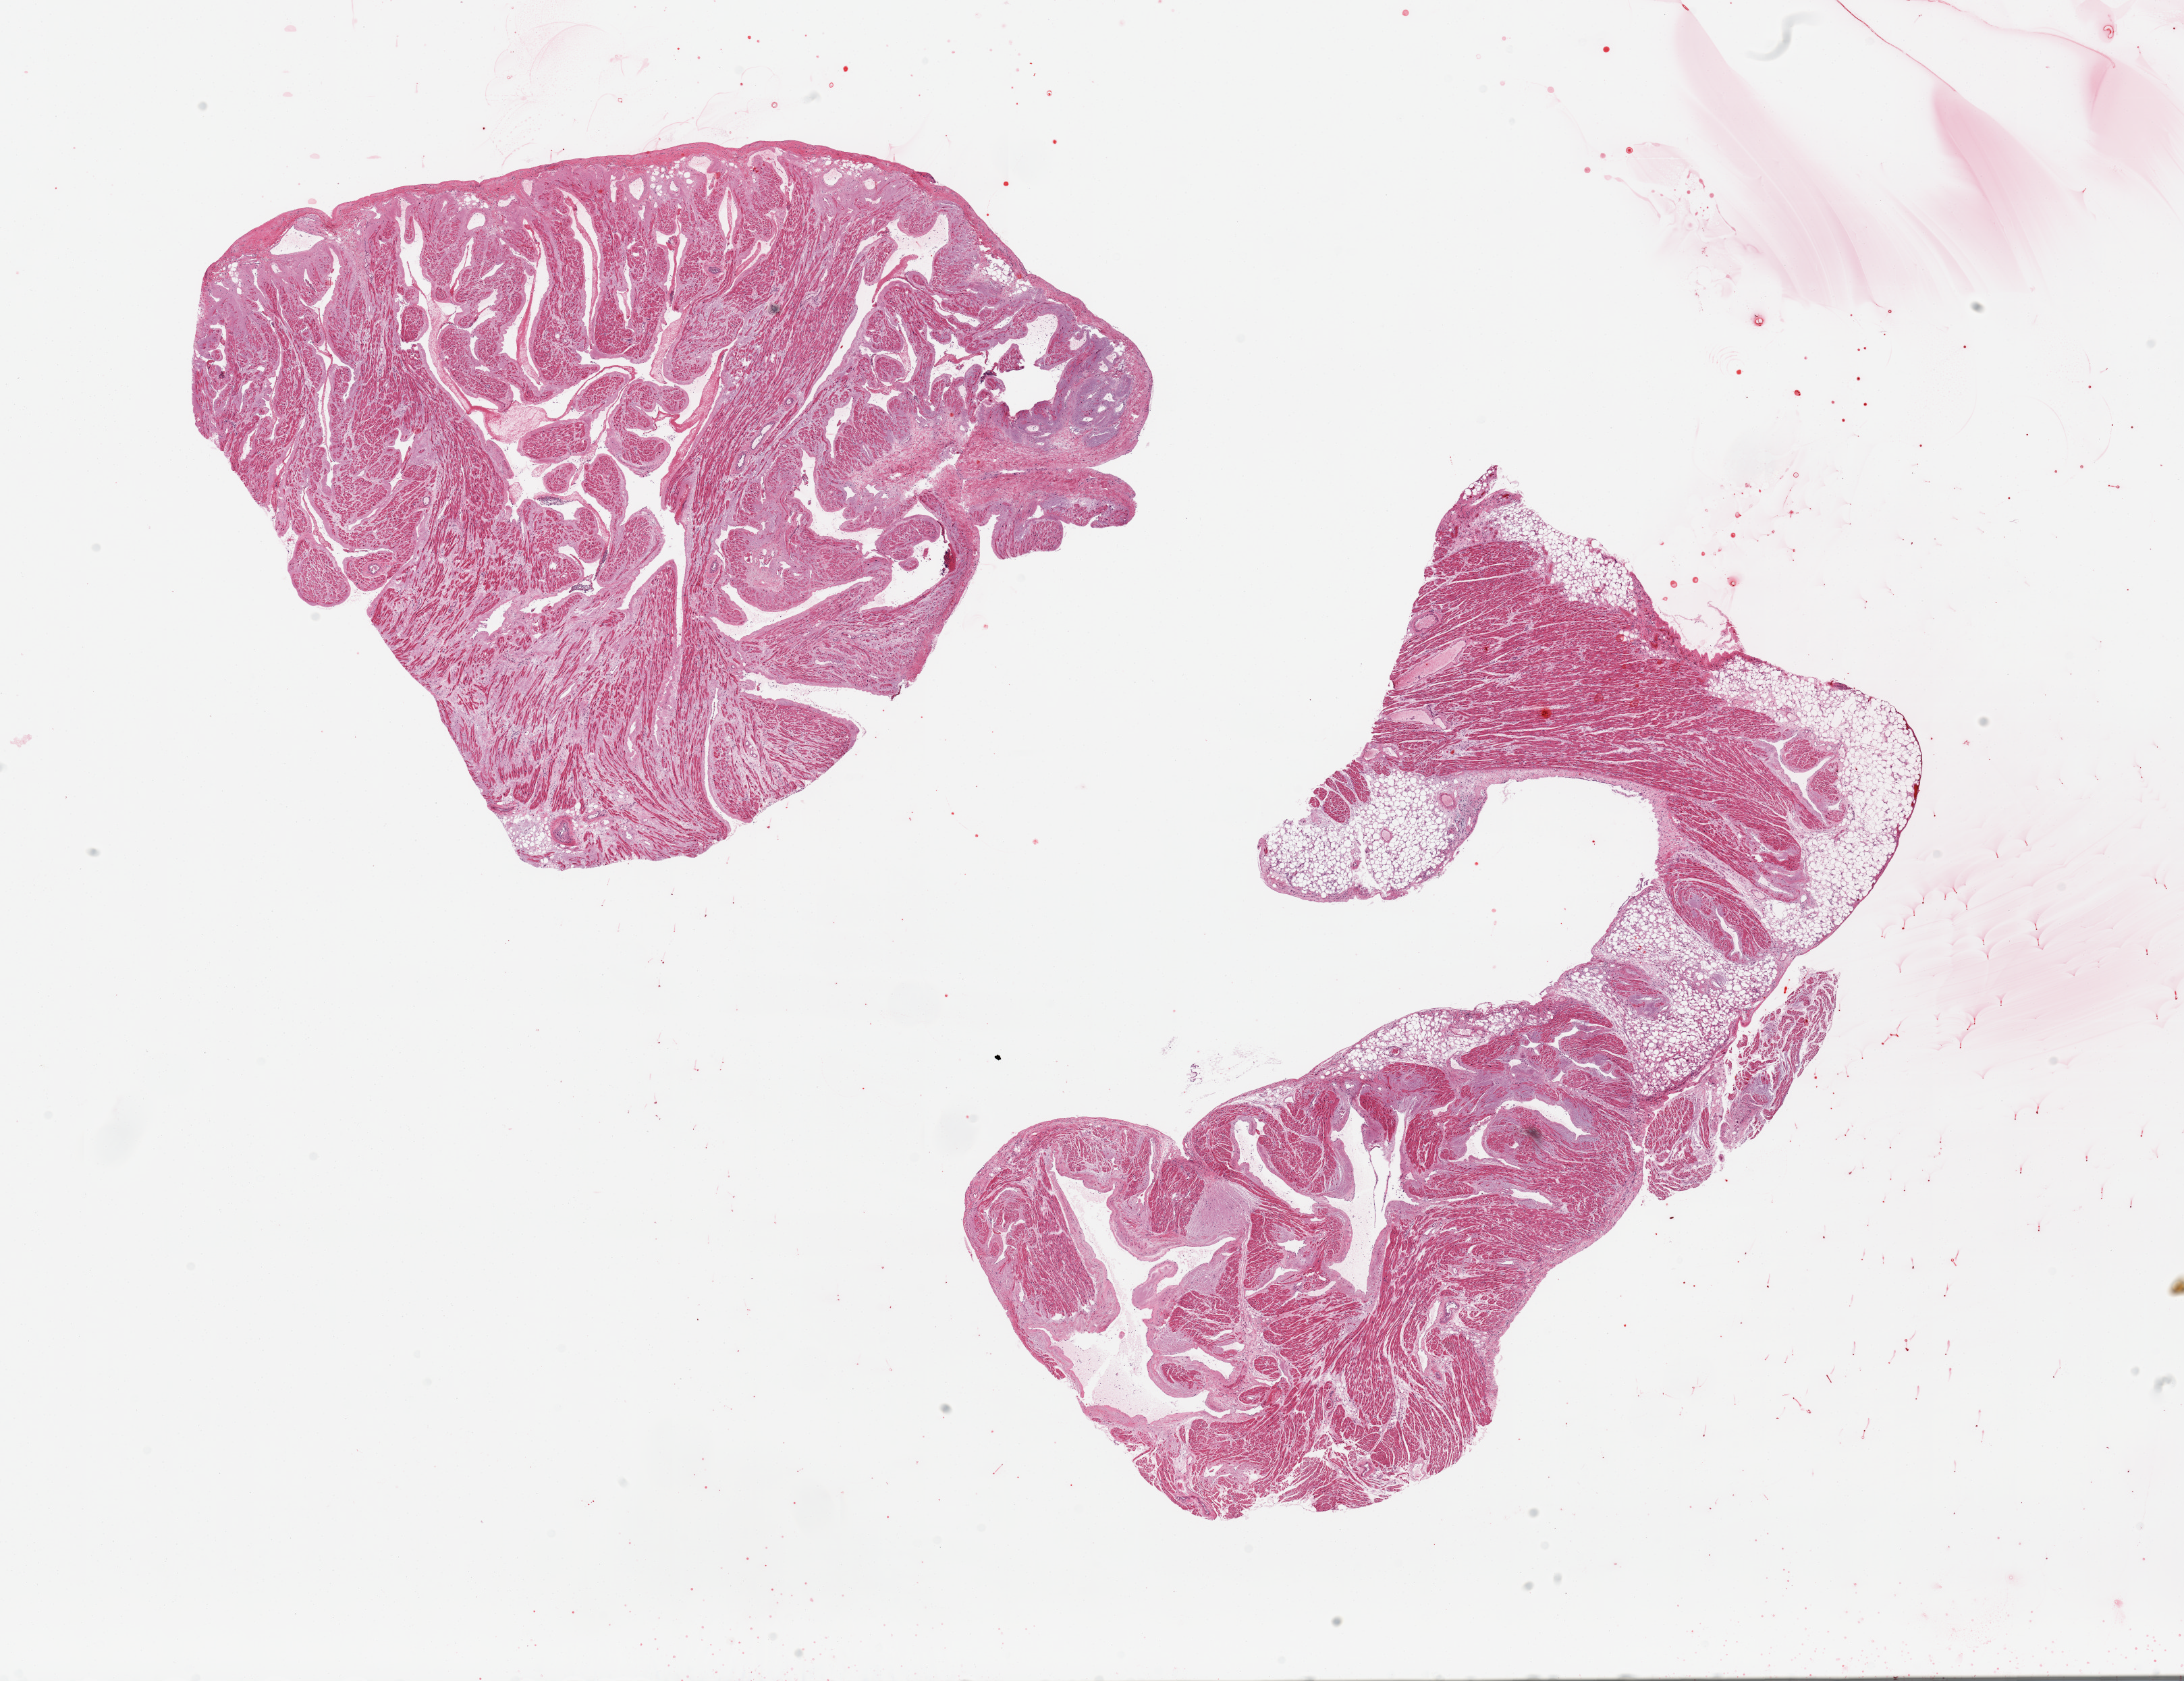
Whole-slide image, H&E stain, brightfield — low-resolution overview of the scanned area, about 25.6 x 19.7 mm. PAXgene-fixed, paraffin-embedded tissue. Section of auricular appendage (target tissue). Donor tissue sample. Donor sex: male.
Reviewer comment on this tissue sample: 2 pieces, no abnormality.